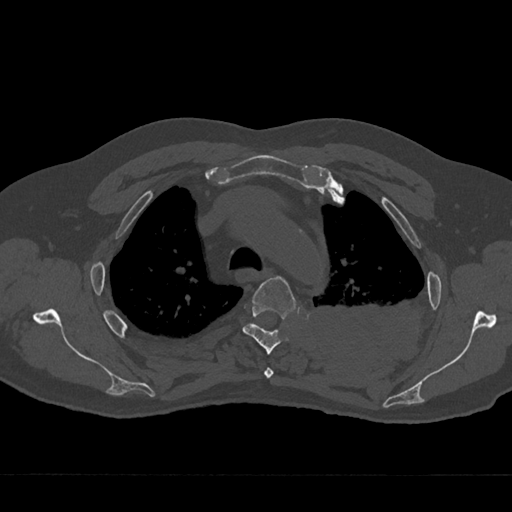
CT including the spine, one axial slice; slice 524 of 797 in the series (ordered by position); reconstruction kernel Br40s/3; bone window (W 1800 / L 400 HU); 0.5 mm slice thickness; 512 × 512 image matrix, field of view 377 × 377 mm. Patient: male, 75 years. From the clinical record (not read from this slice): primary cancer: renal; vertebrae with lytic lesions (as recorded): T4.
Outlined on this slice (semi-automatic segmentation, software-assisted and operator-edited):
- T3 vertebra: bounding box <264,368,274,378> (left, top, right, bottom; pixels)
- T4 vertebra: <243,276,296,355>